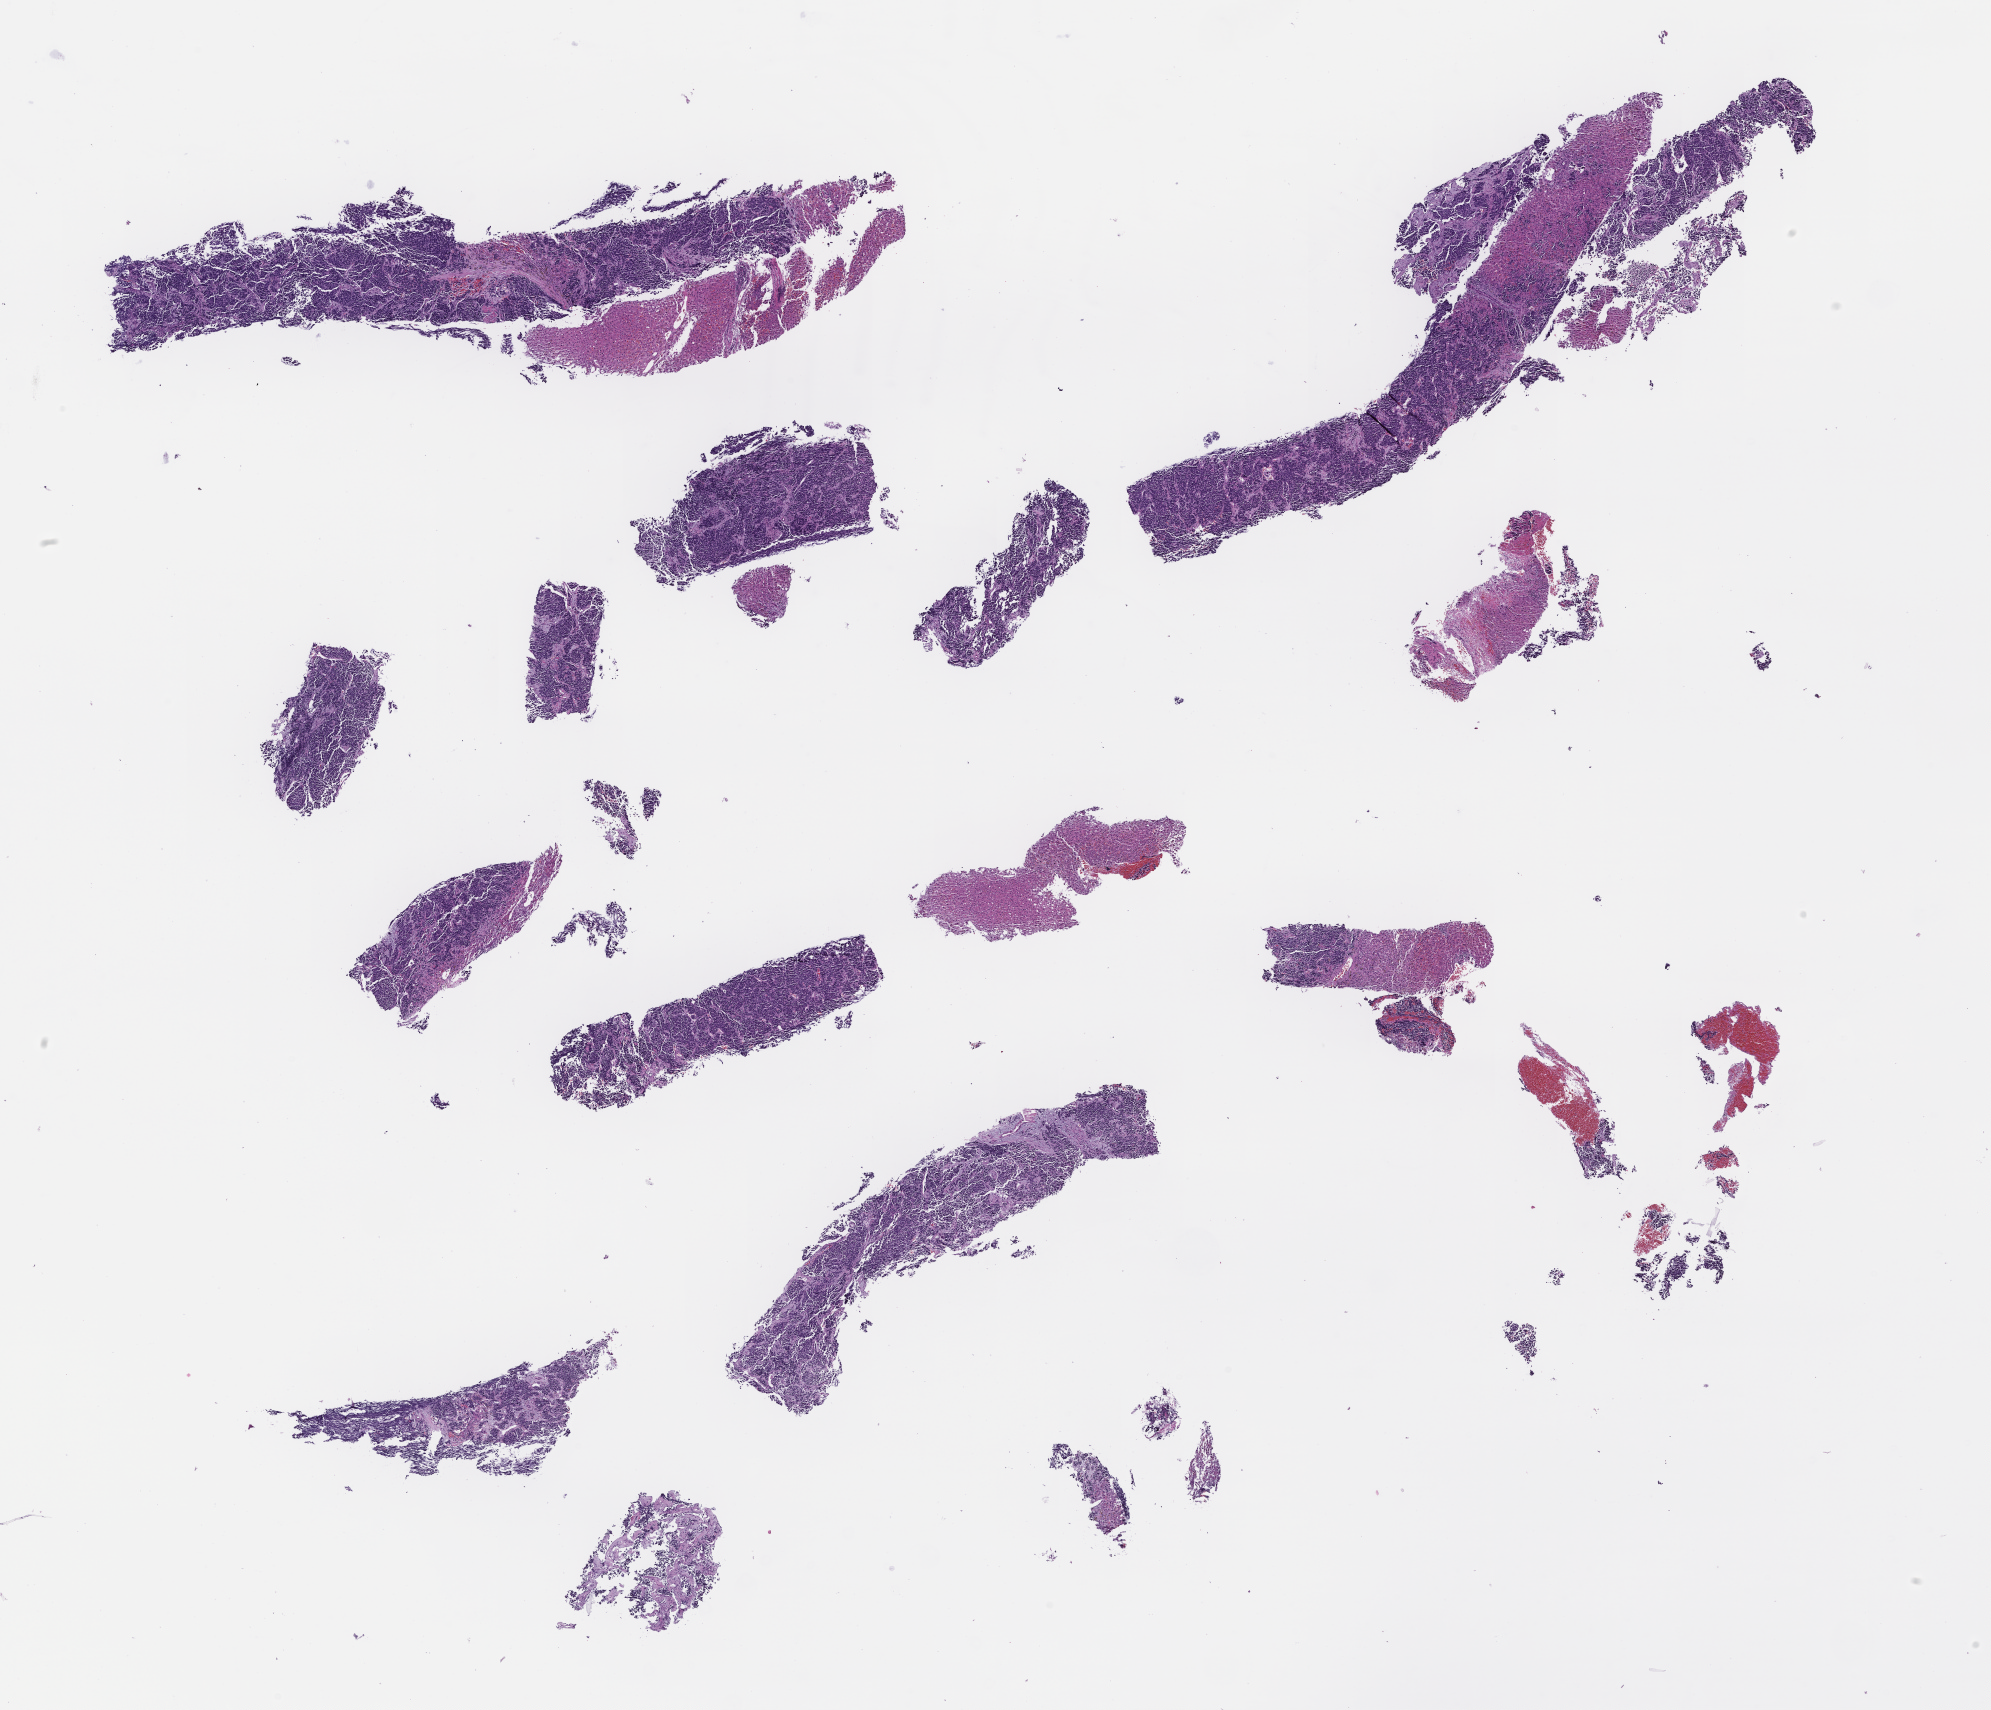
Whole-slide image, H&E stain, shown as a low-resolution overview of the whole scanned area (about 16.1 x 13.8 mm); formalin-fixed, paraffin-embedded (FFPE) tissue. Male patient.
This section: metastatic tumor tissue. Patient diagnosis (primary): Non-Small Cell Lung Carcinoma.